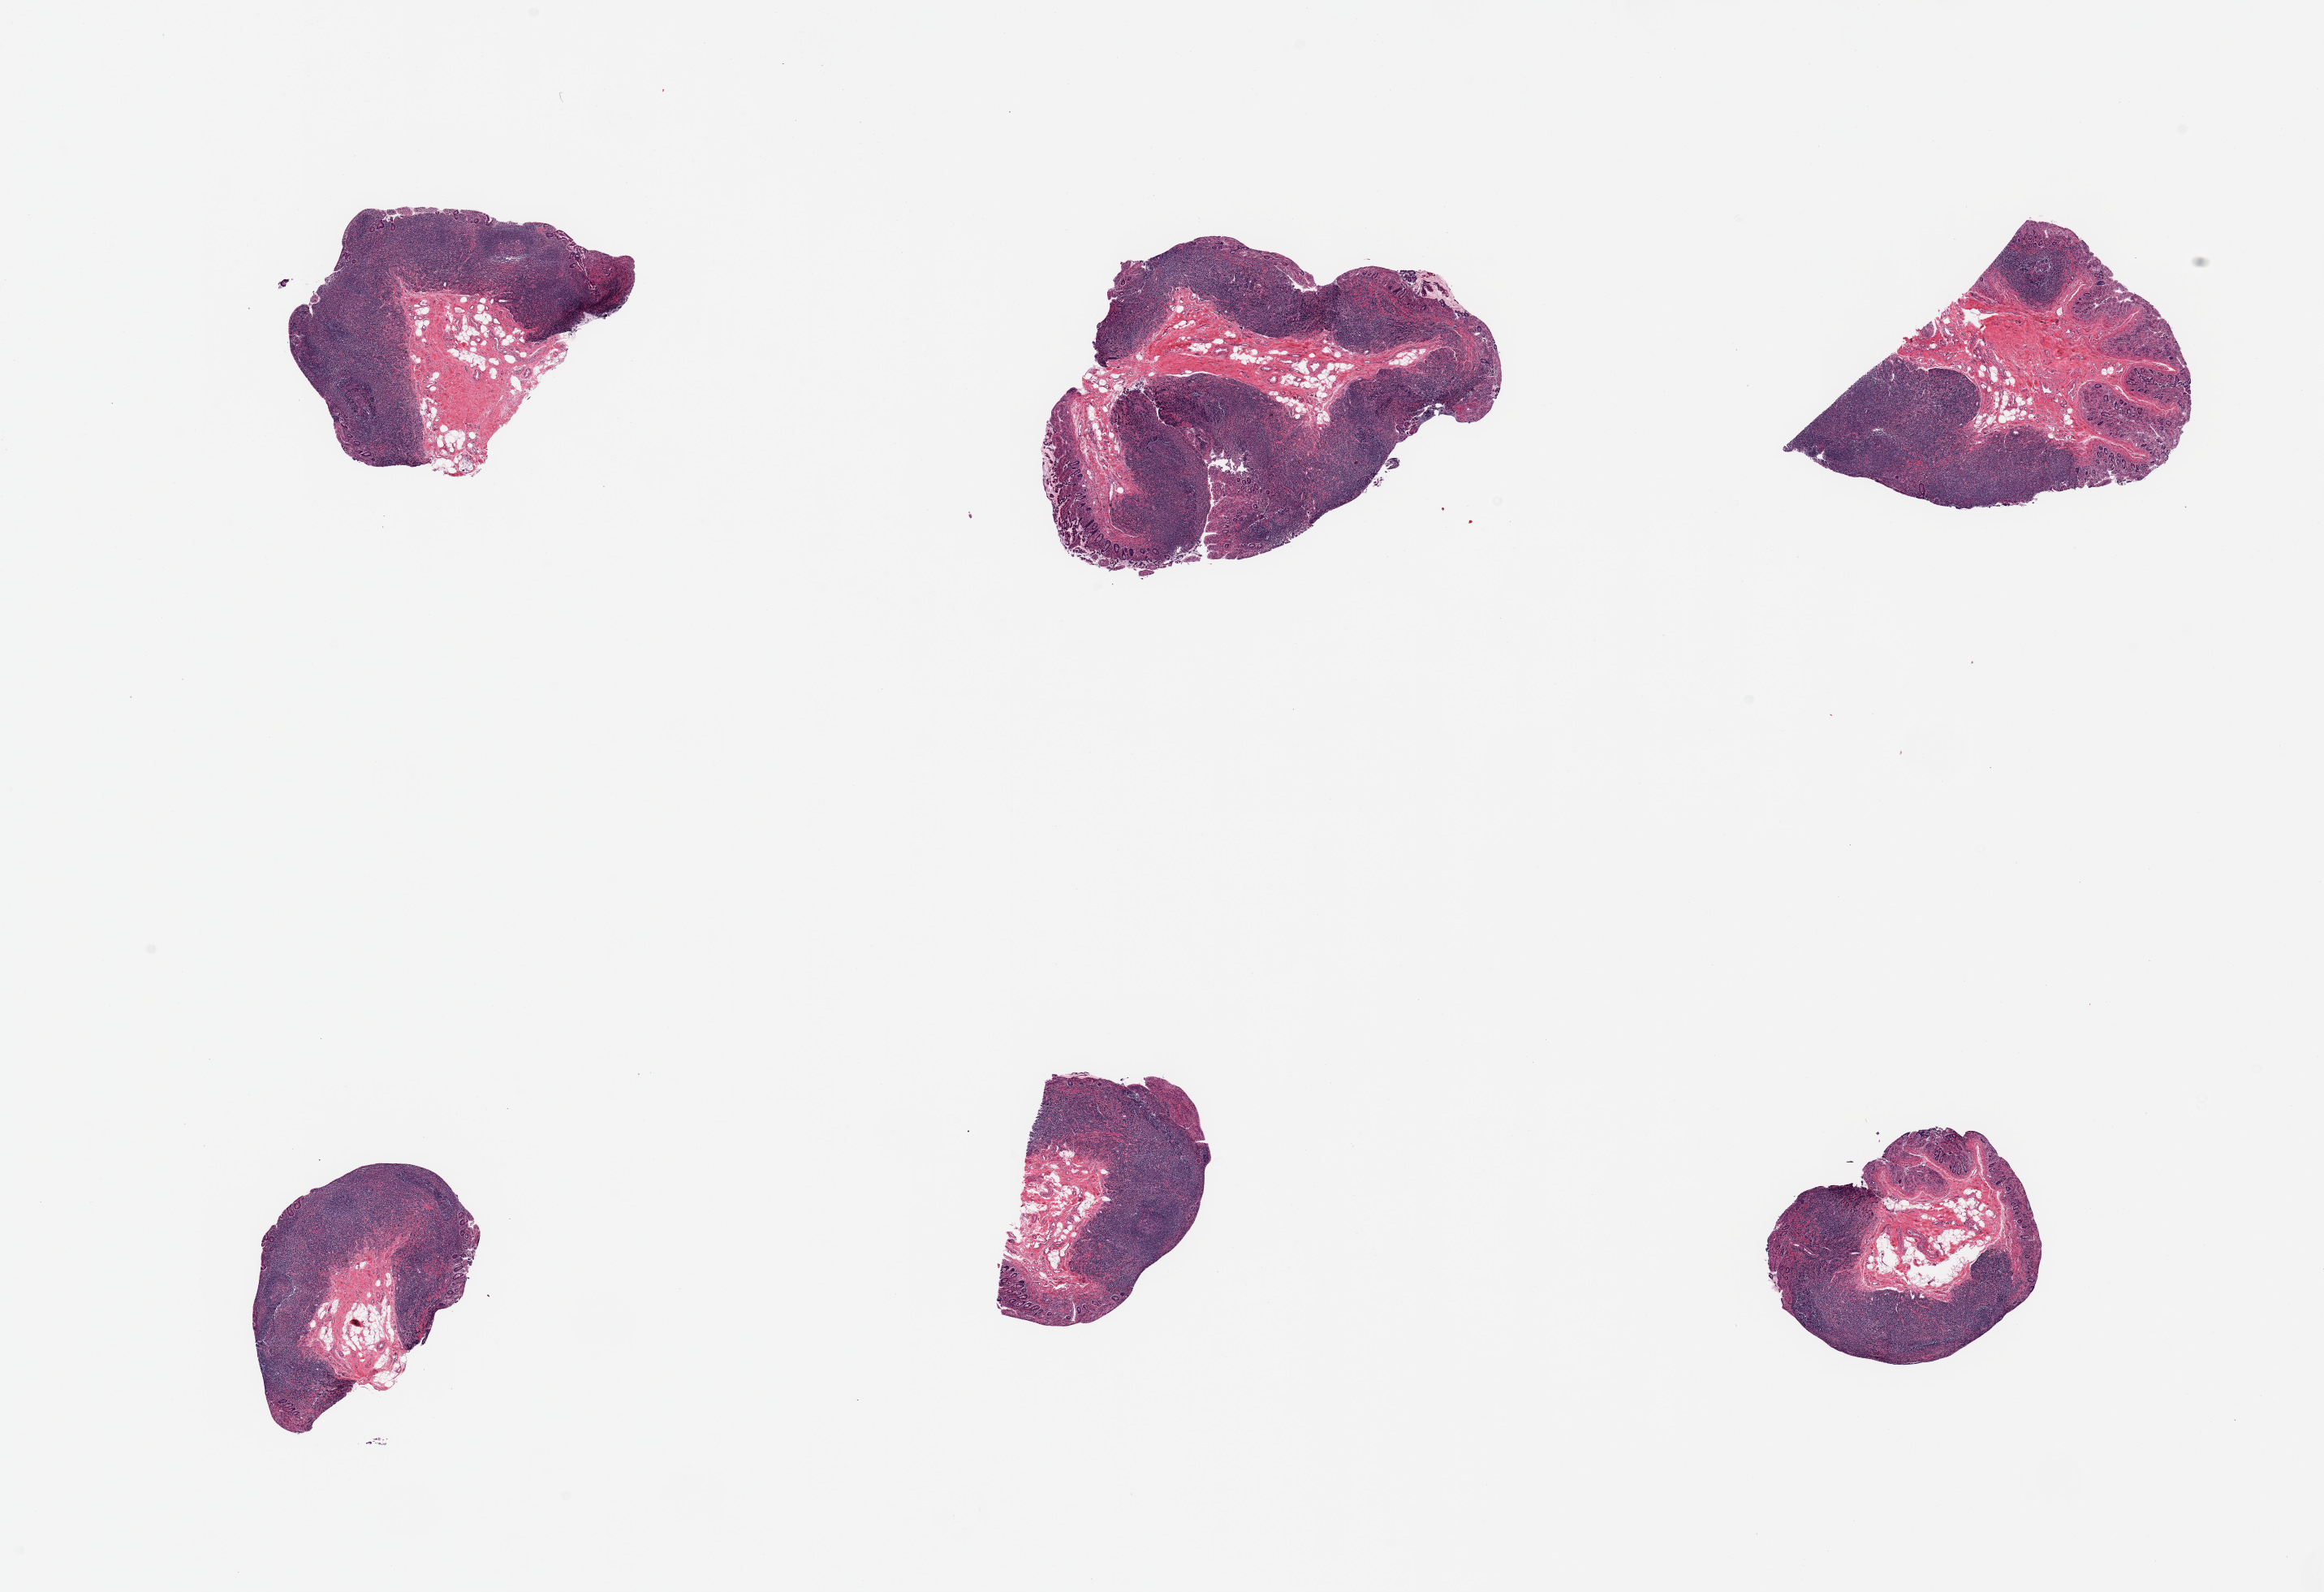
Whole-slide image, haematoxylin and eosin stain — shown as a low-resolution overview of the whole scanned area (about 22.6 x 15.5 mm). PAXgene-fixed paraffin-embedded (PFPE) section. Section of ileum (target tissue). Tissue donor sample. Donor: male.
* review note (as recorded): 6 pieces, abundant well preserved lymphoid/Peyer aggregates are ~50% total tissue